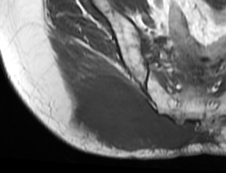
MRI of an extremity soft-tissue mass, one axial slice. Position 45 of 73 along the scan axis. MR volume resampled by the dataset authors to the PET/CT grid (not the native acquisition matrix). 3.27 mm slice thickness. 226 × 173 image matrix, field of view 221 × 169 mm. Female patient. From the clinical record (not read from this slice): histological type: spindle cell suggestive of myxofibrosarcoma; grade: intermediate; site of the primary tumour: right buttock.
Annotated regions visible in this slice (expert contour drawn on MRI and transferred to this co-registered scan by the dataset authors):
- gross tumour volume (mass): box from (x=66, y=76) to (x=190, y=150) px